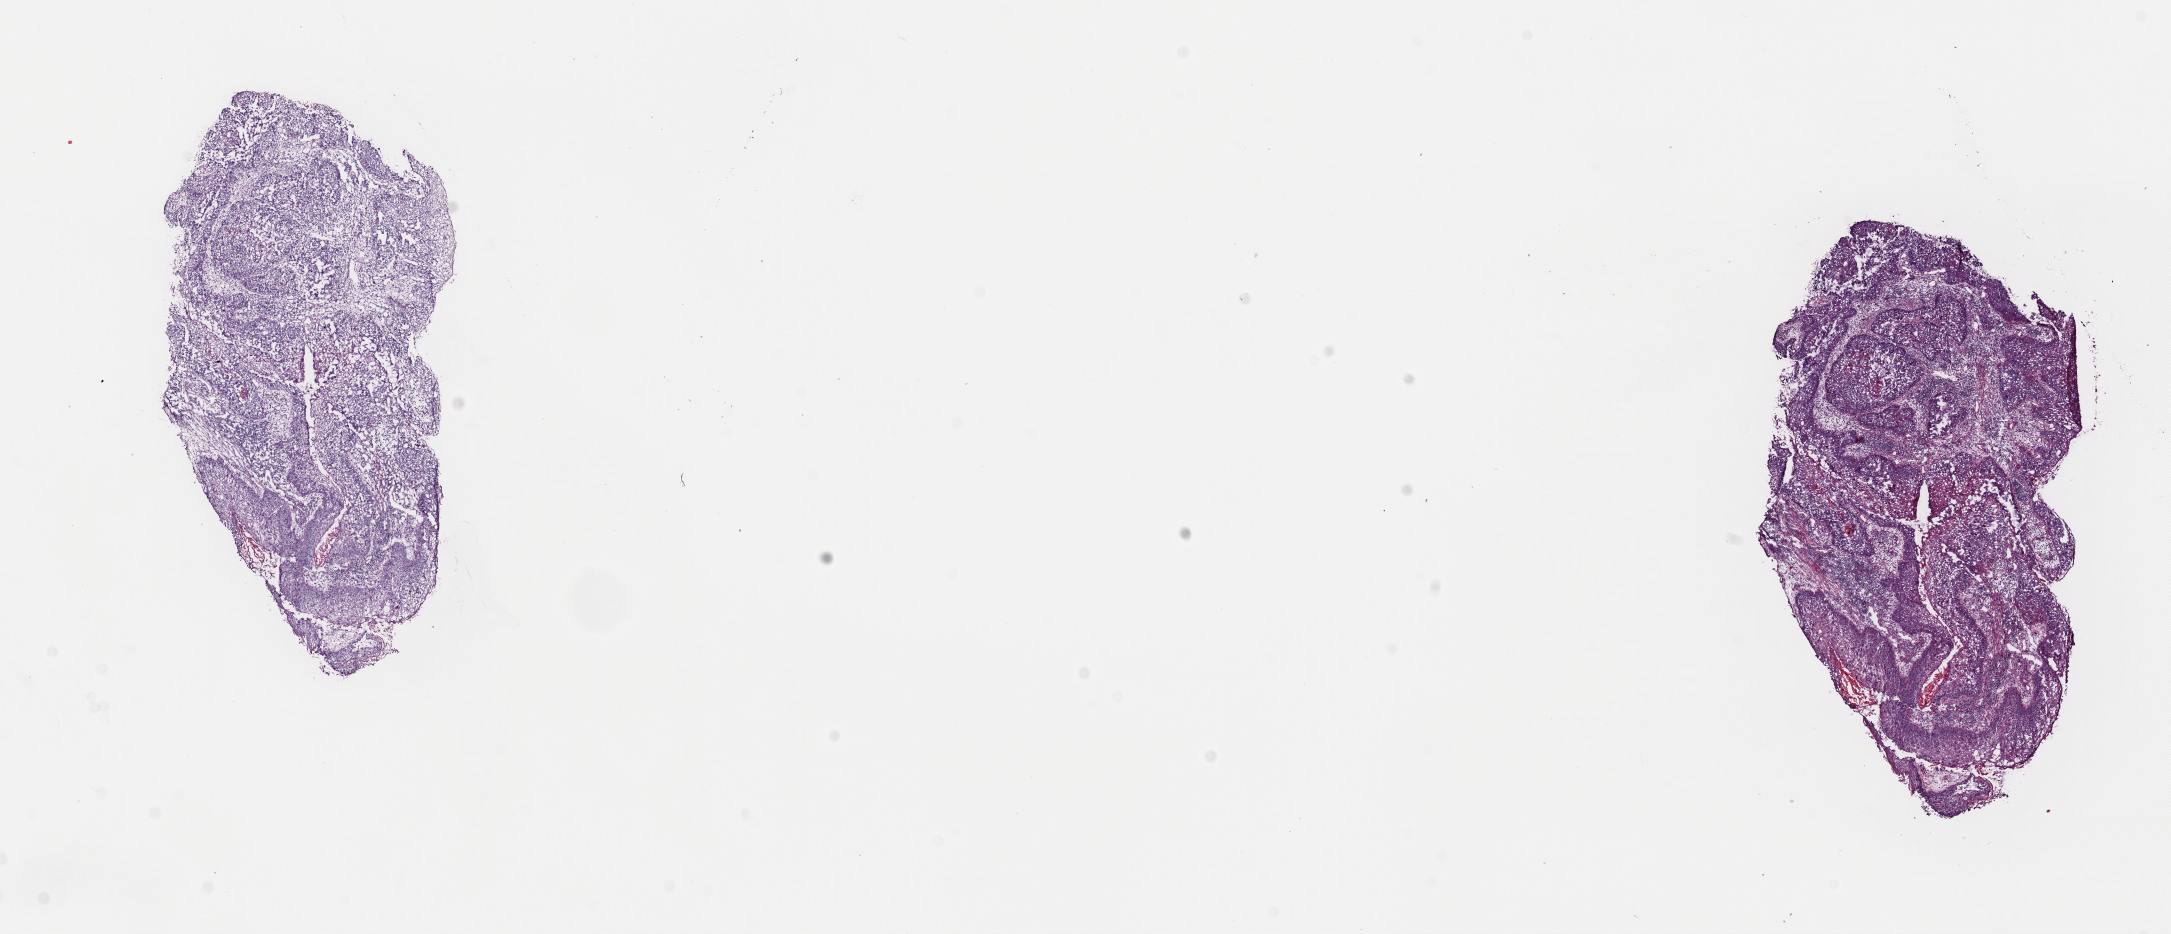
Whole-slide histology image, Hematoxylin and eosin (H&E) stained, shown as a low-resolution overview of the whole scanned area (about 17.2 x 7.4 mm, slide scanned at 40x). Frozen section. Primary tumour sample from the lung. Female patient; age at initial diagnosis 71 years. Slide review estimates, as recorded: tumour cells 100%, tumour nuclei 80%, normal cells 0%, stromal cells 0%, necrosis 0%. Inflammatory infiltration, as recorded: lymphocyte infiltration 3%, monocyte infiltration 1%, neutrophil infiltration 0%.
AJCC pathologic stage: IA (7th edition). Pathologic diagnosis: Squamous cell carcinoma, NOS. TNM: T1b N0 M0.